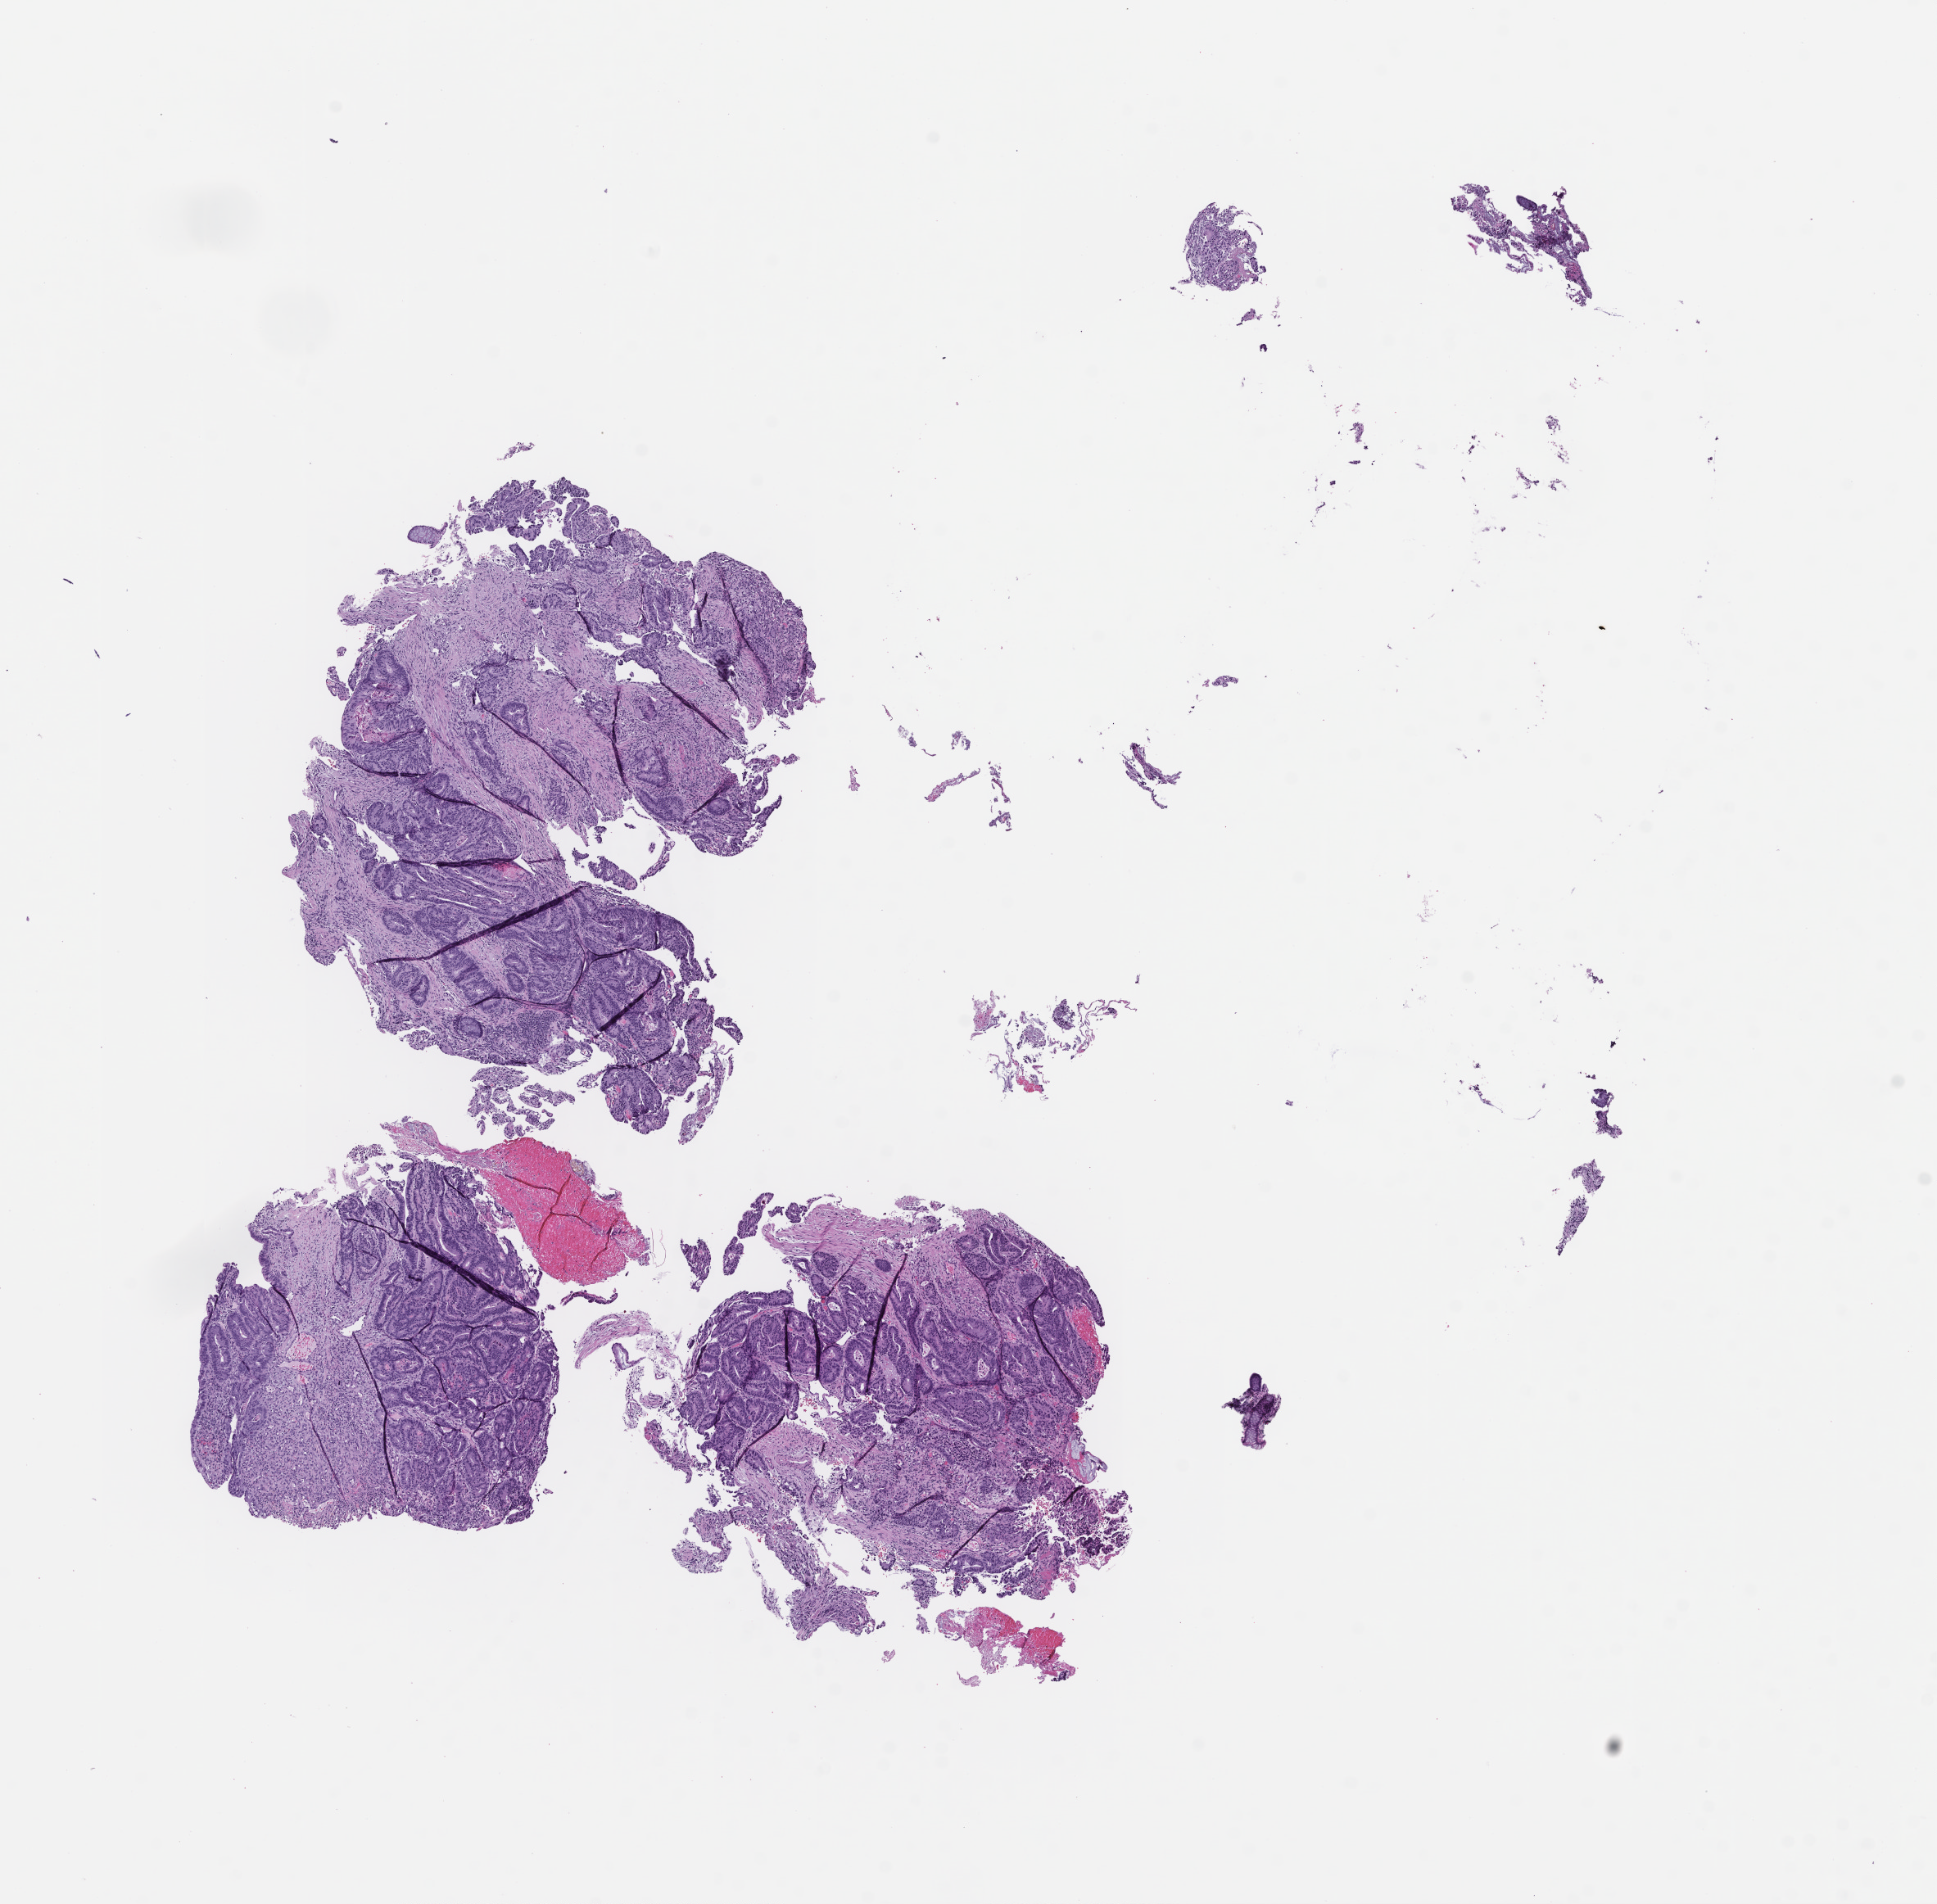
Whole-slide image, haematoxylin and eosin stain — a low-resolution overview of the entire scanned area, about 9.5 x 9.4 mm. FFPE section. Tissue site: colon. Specimen time point: archival tissue. Patient sex: male.
This section: primary tumour tissue. Diagnosis: Colorectal Carcinoma.